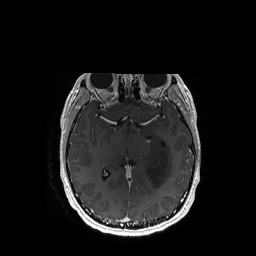
Brain MRI from a brain-tumour surgery series, one axial slice; position 98 of 192 along the scan axis; T1-weighted post-contrast; 1 mm slice thickness; 256 × 256 image matrix, field of view 256 × 256 mm. Case-level facts recorded for this patient, not image findings: histopathology: Astrocytoma; WHO grade: 3; IDH mutation: yes; tumour location: Left Temporal.
Outlined on this slice (expert manual segmentation):
- tumour: bounding box (x1, y1, x2, y2) in pixels: (146, 145, 171, 188)